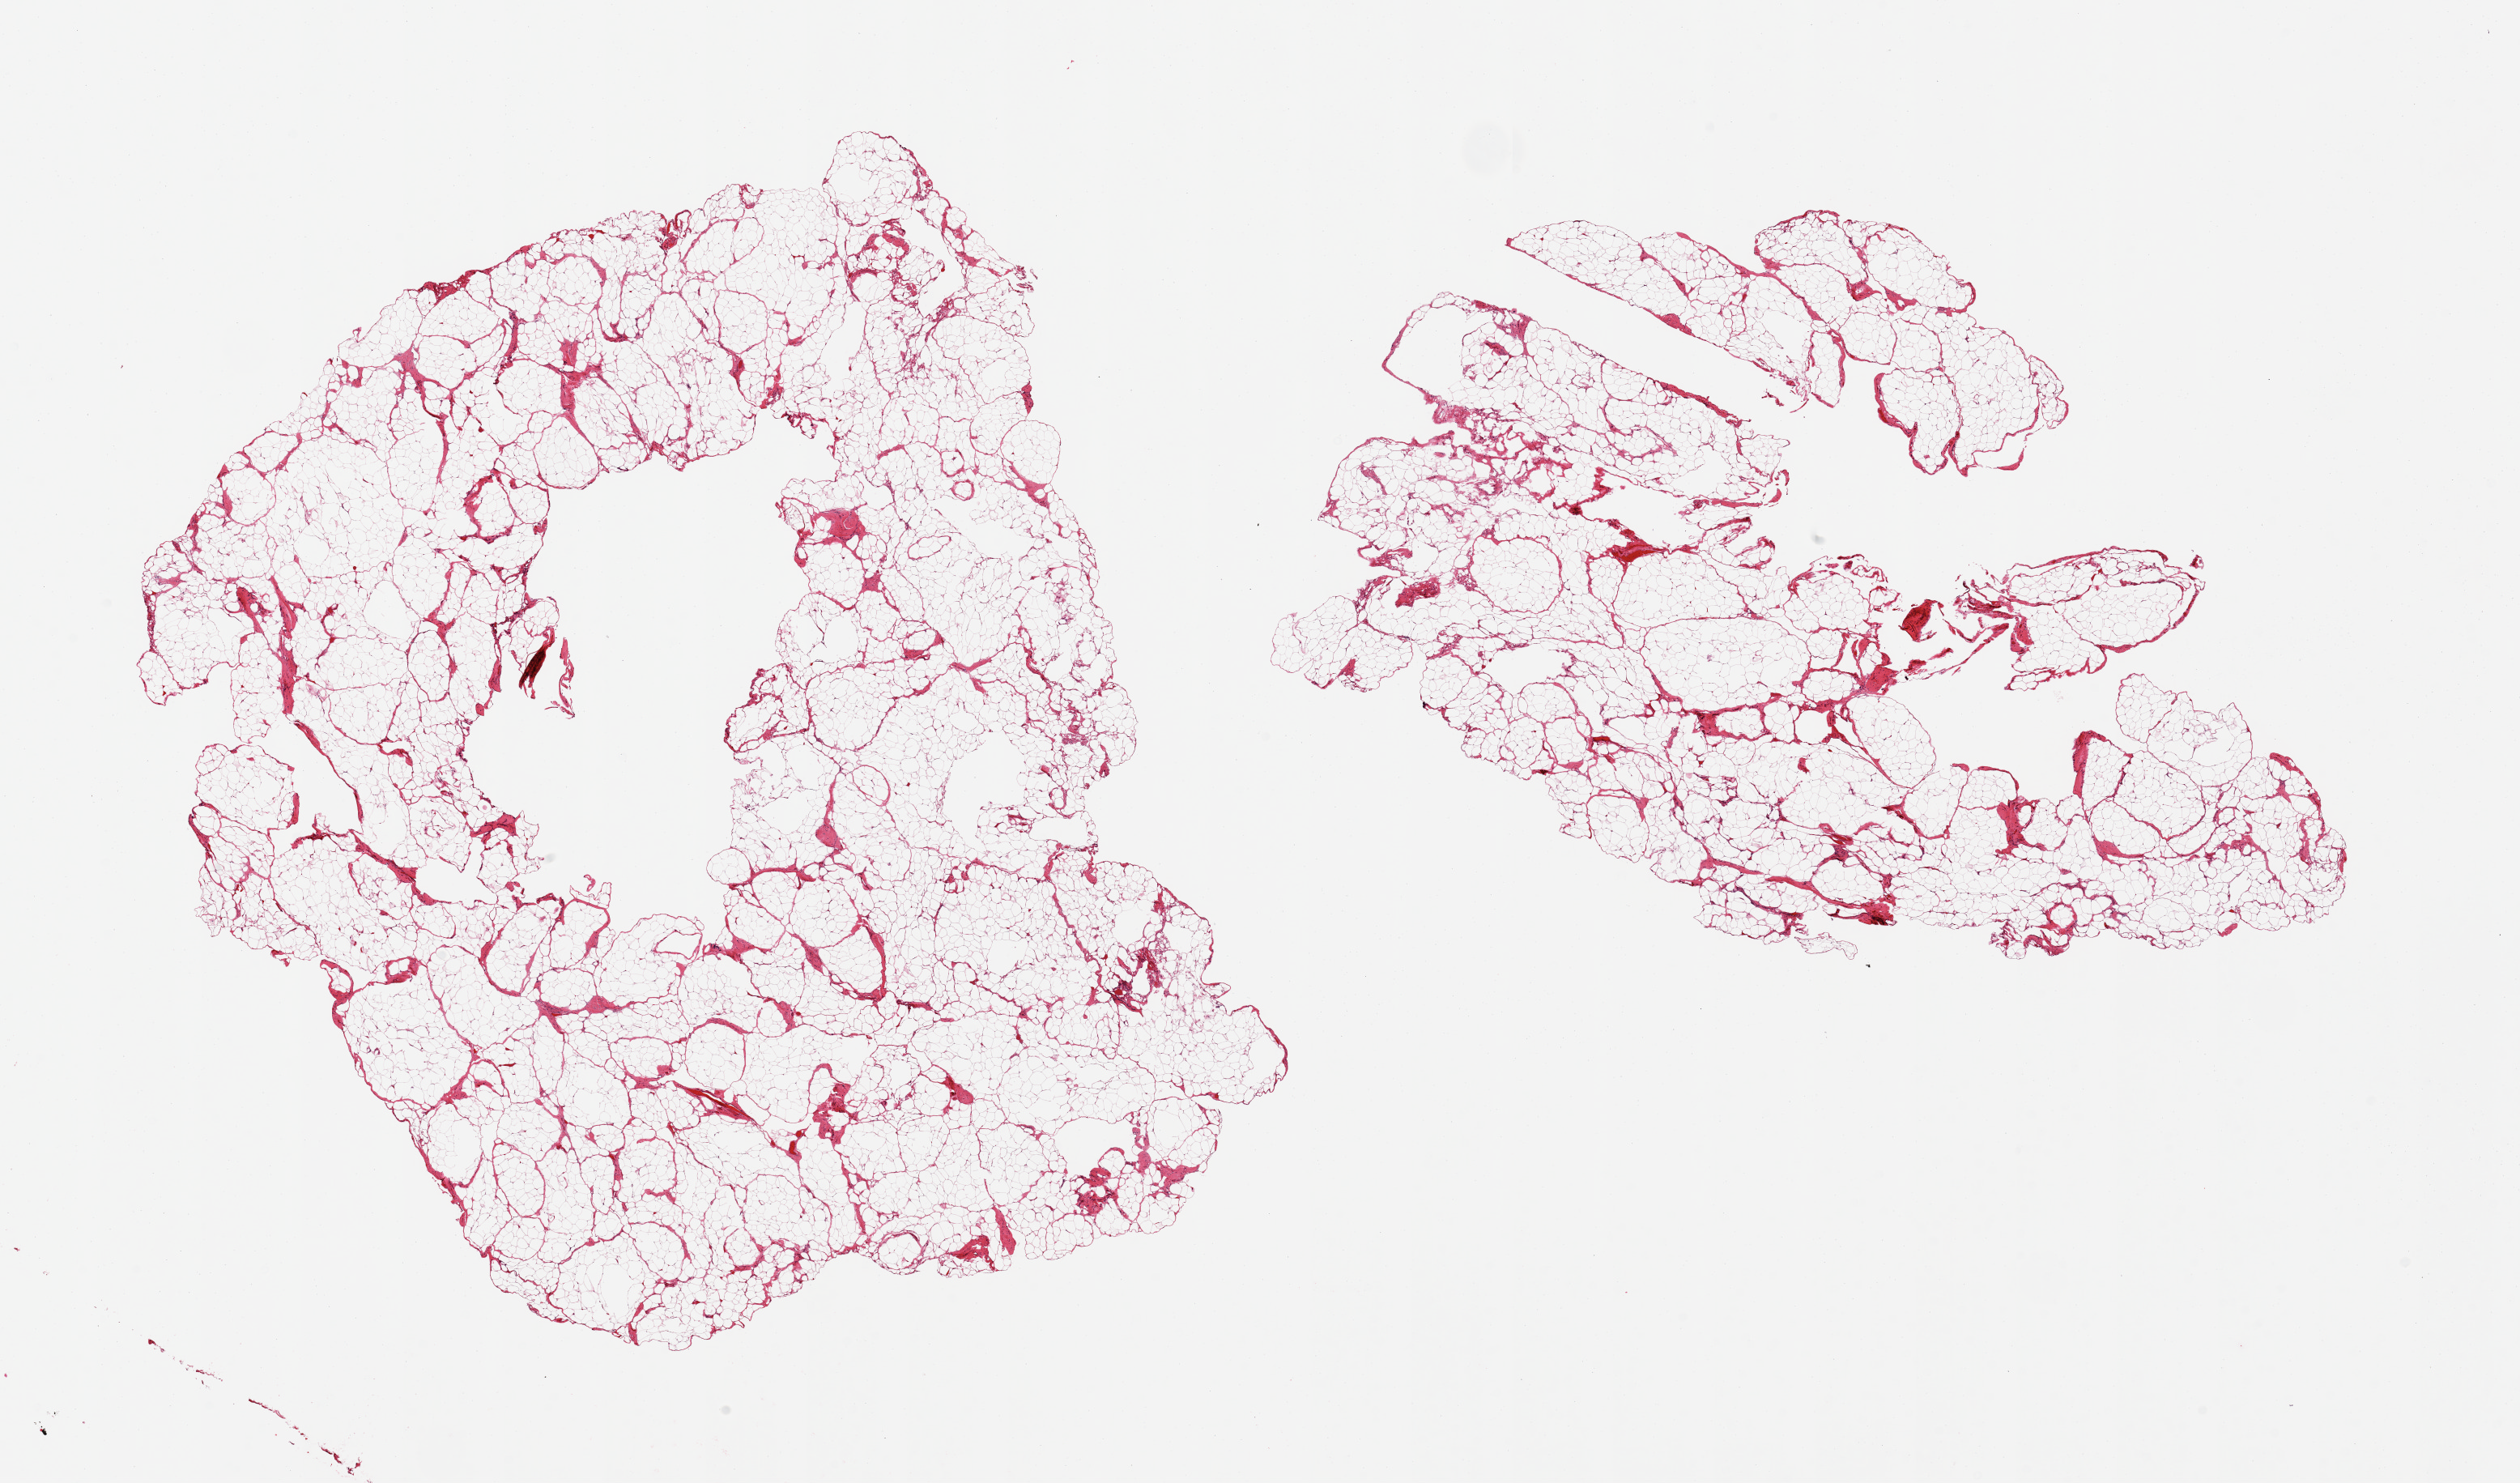
Digitized haematoxylin and eosin-stained section, shown as a low-resolution overview of the whole scanned area (about 24.6 x 14.5 mm); PAXgene-fixed, paraffin-embedded tissue; sampled site (target tissue): omentum; donor tissue sample. Male donor.
Reviewer comment on this tissue sample: 2 pieces.